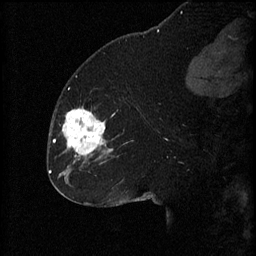
Breast MRI (dynamic contrast-enhanced), one sagittal slice; position 26 of 60 along the scan axis; 3 images stored at this slice position (order not interpretable as contrast timing); 1.5 T; TE 4.2 ms, TR 8.2 ms; 2 mm slice thickness; 256 × 256 image matrix. Patient: female, 32 years.
Structures marked on this image (semi-automatic segmentation, software-assisted and operator-edited):
- analysis volume of interest (the breast-tissue region the enhancement analysis was run in; not a lesion): bounding box <62,106,111,165> (left, top, right, bottom; pixels)
- tumour enhancement mask (voxels above the 70 % enhancement threshold inside the analysis volume of interest): <62,108,105,157>